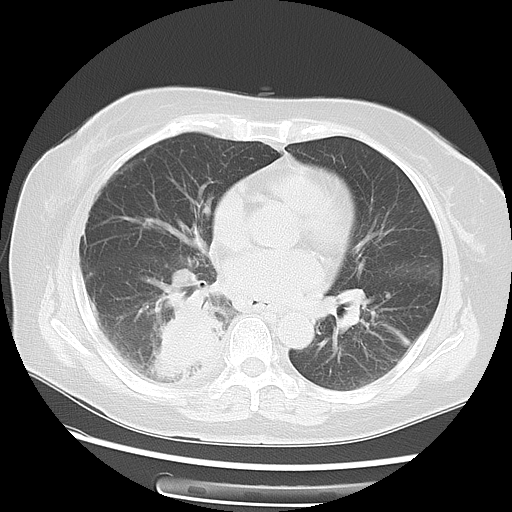
Chest CT, one axial slice. Position 29 of 57 along the scan axis. Lung window (W 1500 / L -600 HU). 512 × 512 image matrix. Female patient, age 69 years. From the clinical record (not read from this slice): clinical TNM (as recorded): T2 N1 M1a.
Outlined on this slice (rectangle marked by the reading radiologist):
- lung tumour (recorded histology: adenocarcinoma): bounding box <137,293,229,393> (left, top, right, bottom; pixels)